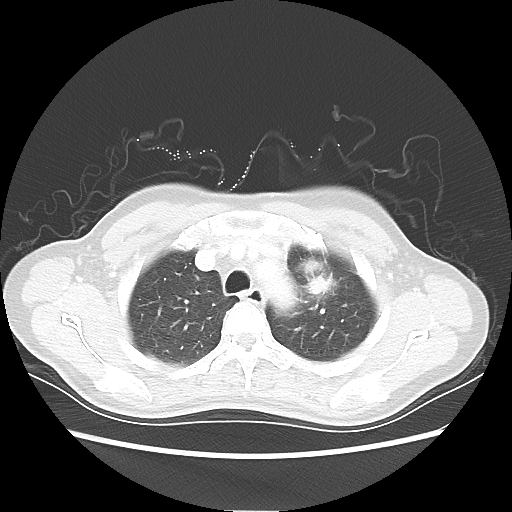
Chest CT, one axial slice. Slice 43 of 54 in the series (ordered by position). Reconstruction kernel LUNG. Lung window (W 1500 / L -600 HU). 5 mm slice thickness. 512 × 512 image matrix, field of view 360 × 360 mm. Female patient, age 53 years. Case-level facts recorded for this patient, not image findings: clinical TNM (as recorded): T1c N0 M0.
Structures marked on this image (rectangle marked by the reading radiologist):
- lung tumour (recorded histology: adenocarcinoma): bounding box [x1, y1, x2, y2] px = [292, 253, 341, 300]
- lung tumour (recorded histology: adenocarcinoma): [298, 256, 339, 295]